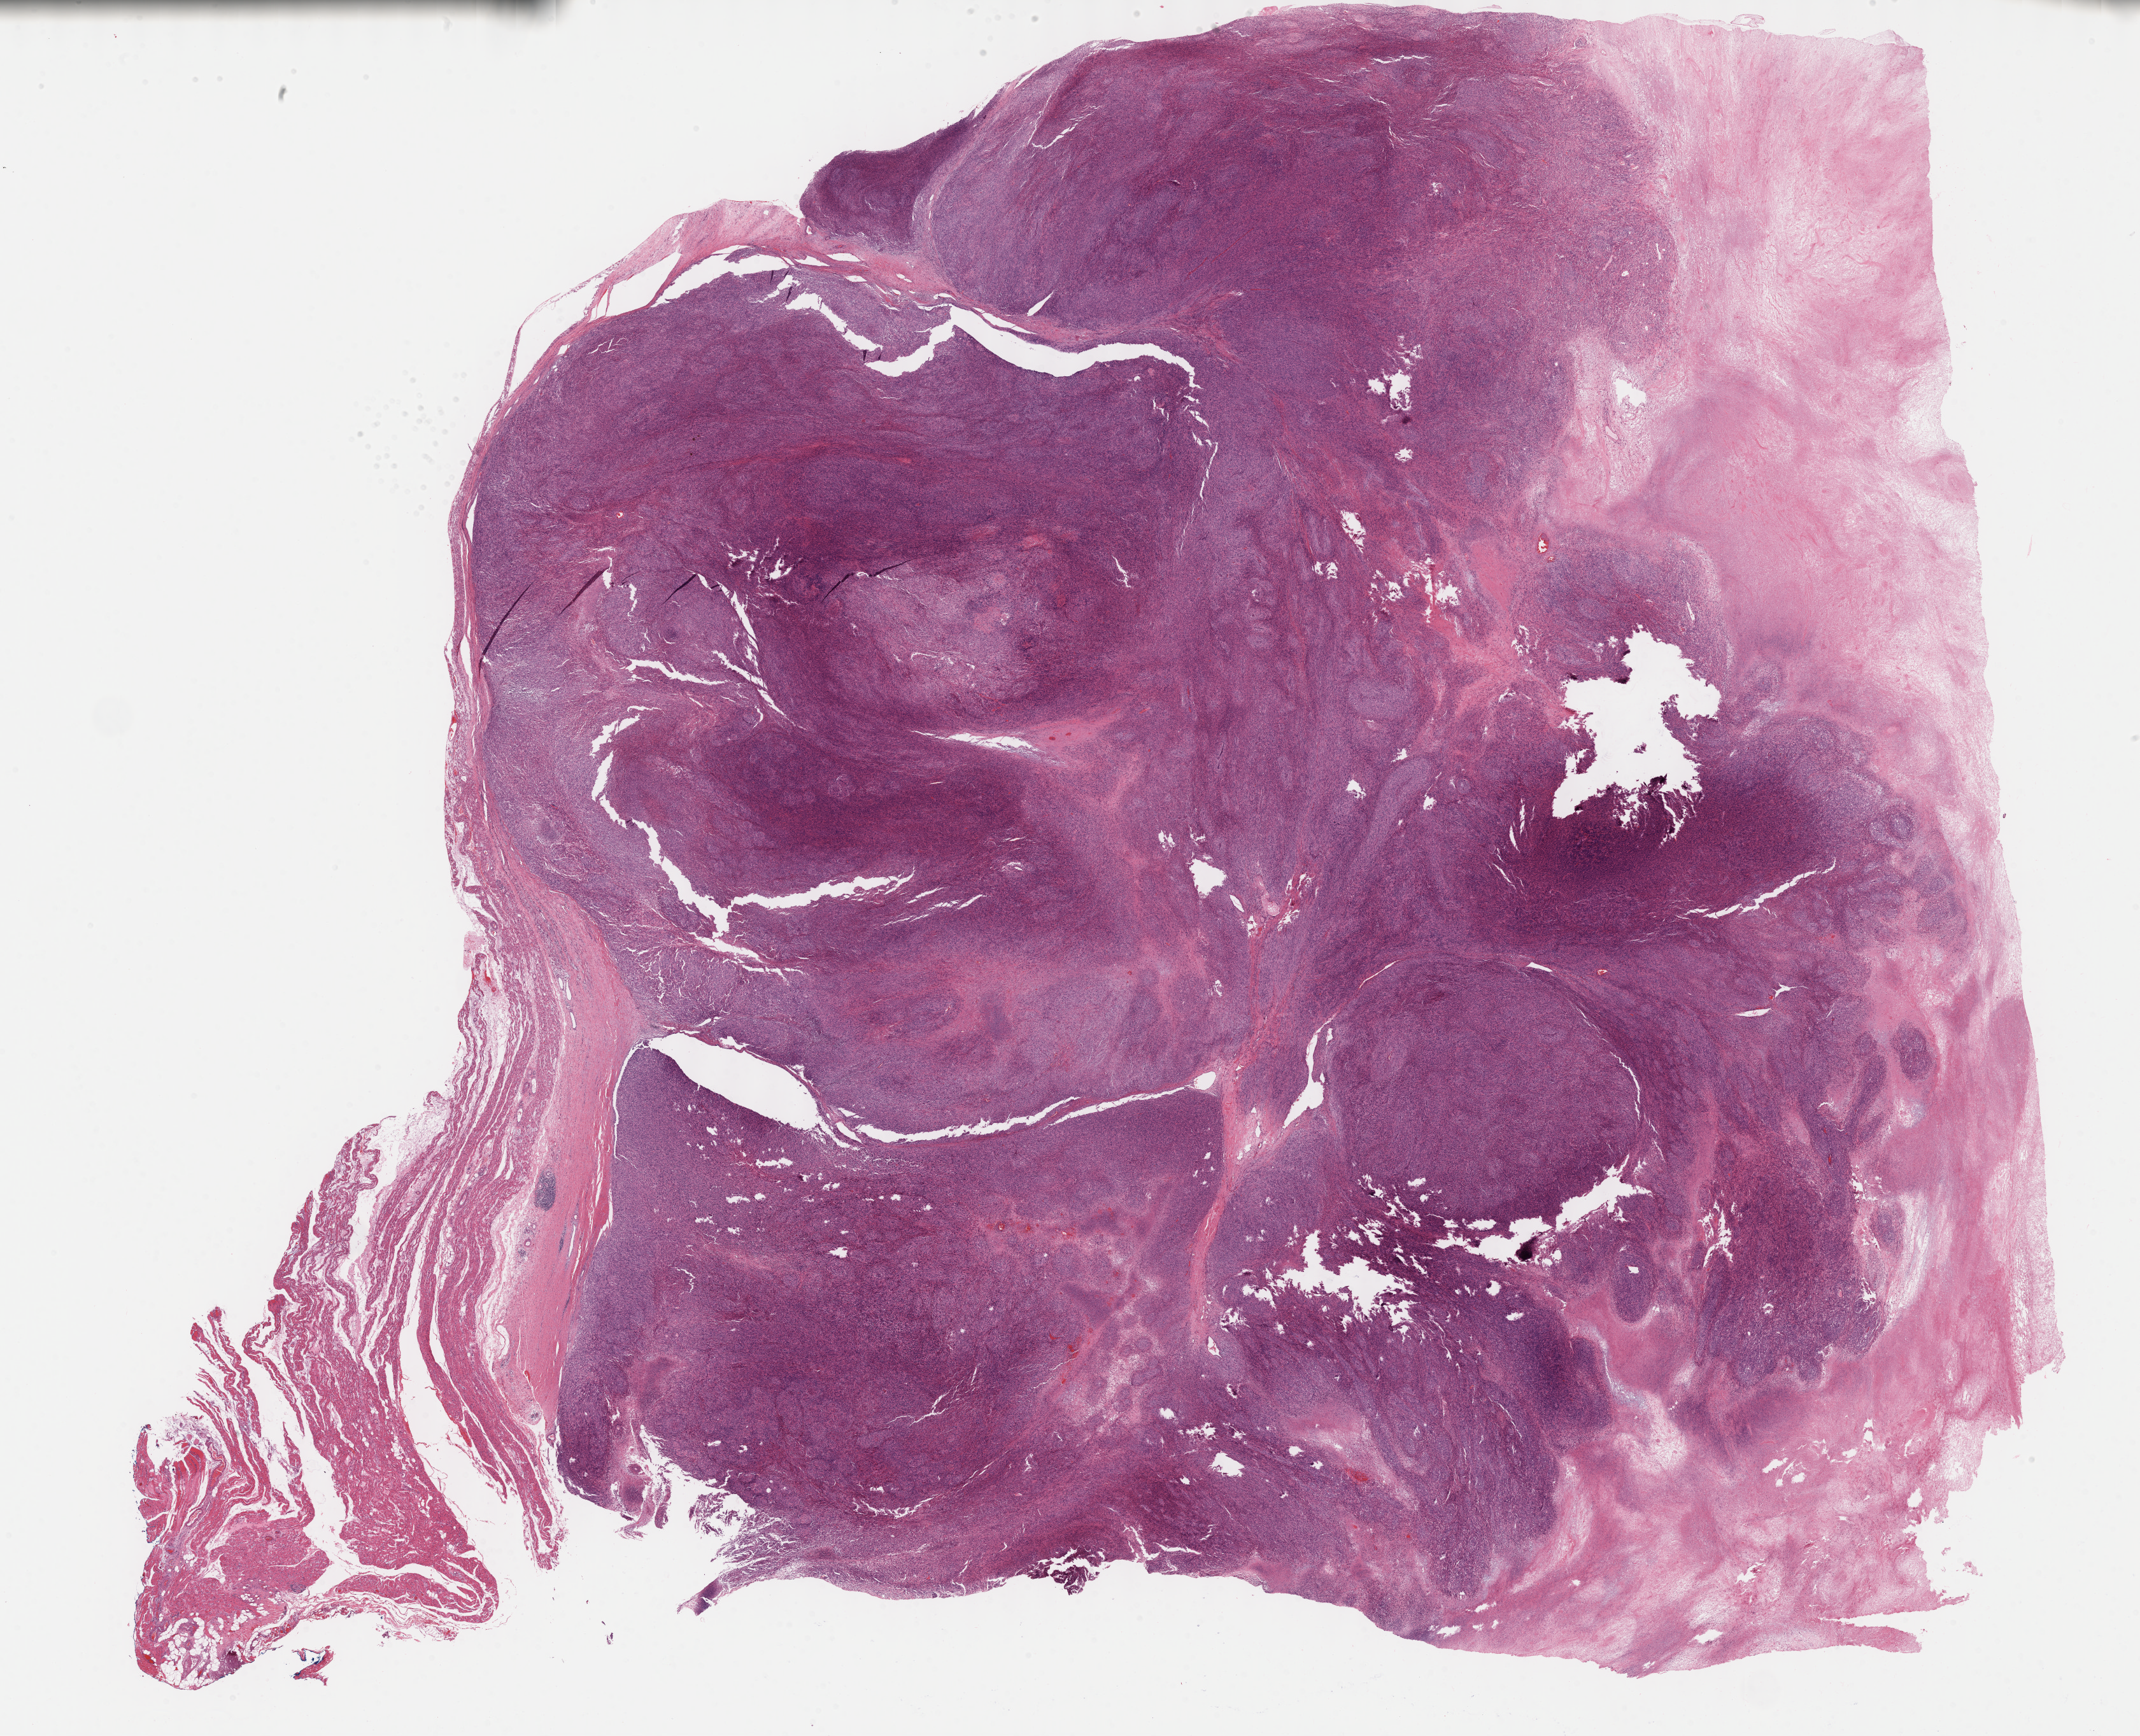
Whole-slide histology image, H&E-stained — shown as a low-resolution overview of the whole scanned area (about 27.2 x 22.1 mm), formalin-fixed paraffin-embedded (FFPE) diagnostic section, primary tumour sample from the retroperitoneum and peritoneum. Male, age 55 years at initial diagnosis.
Diagnosis: Undifferentiated sarcoma (retroperitoneum).